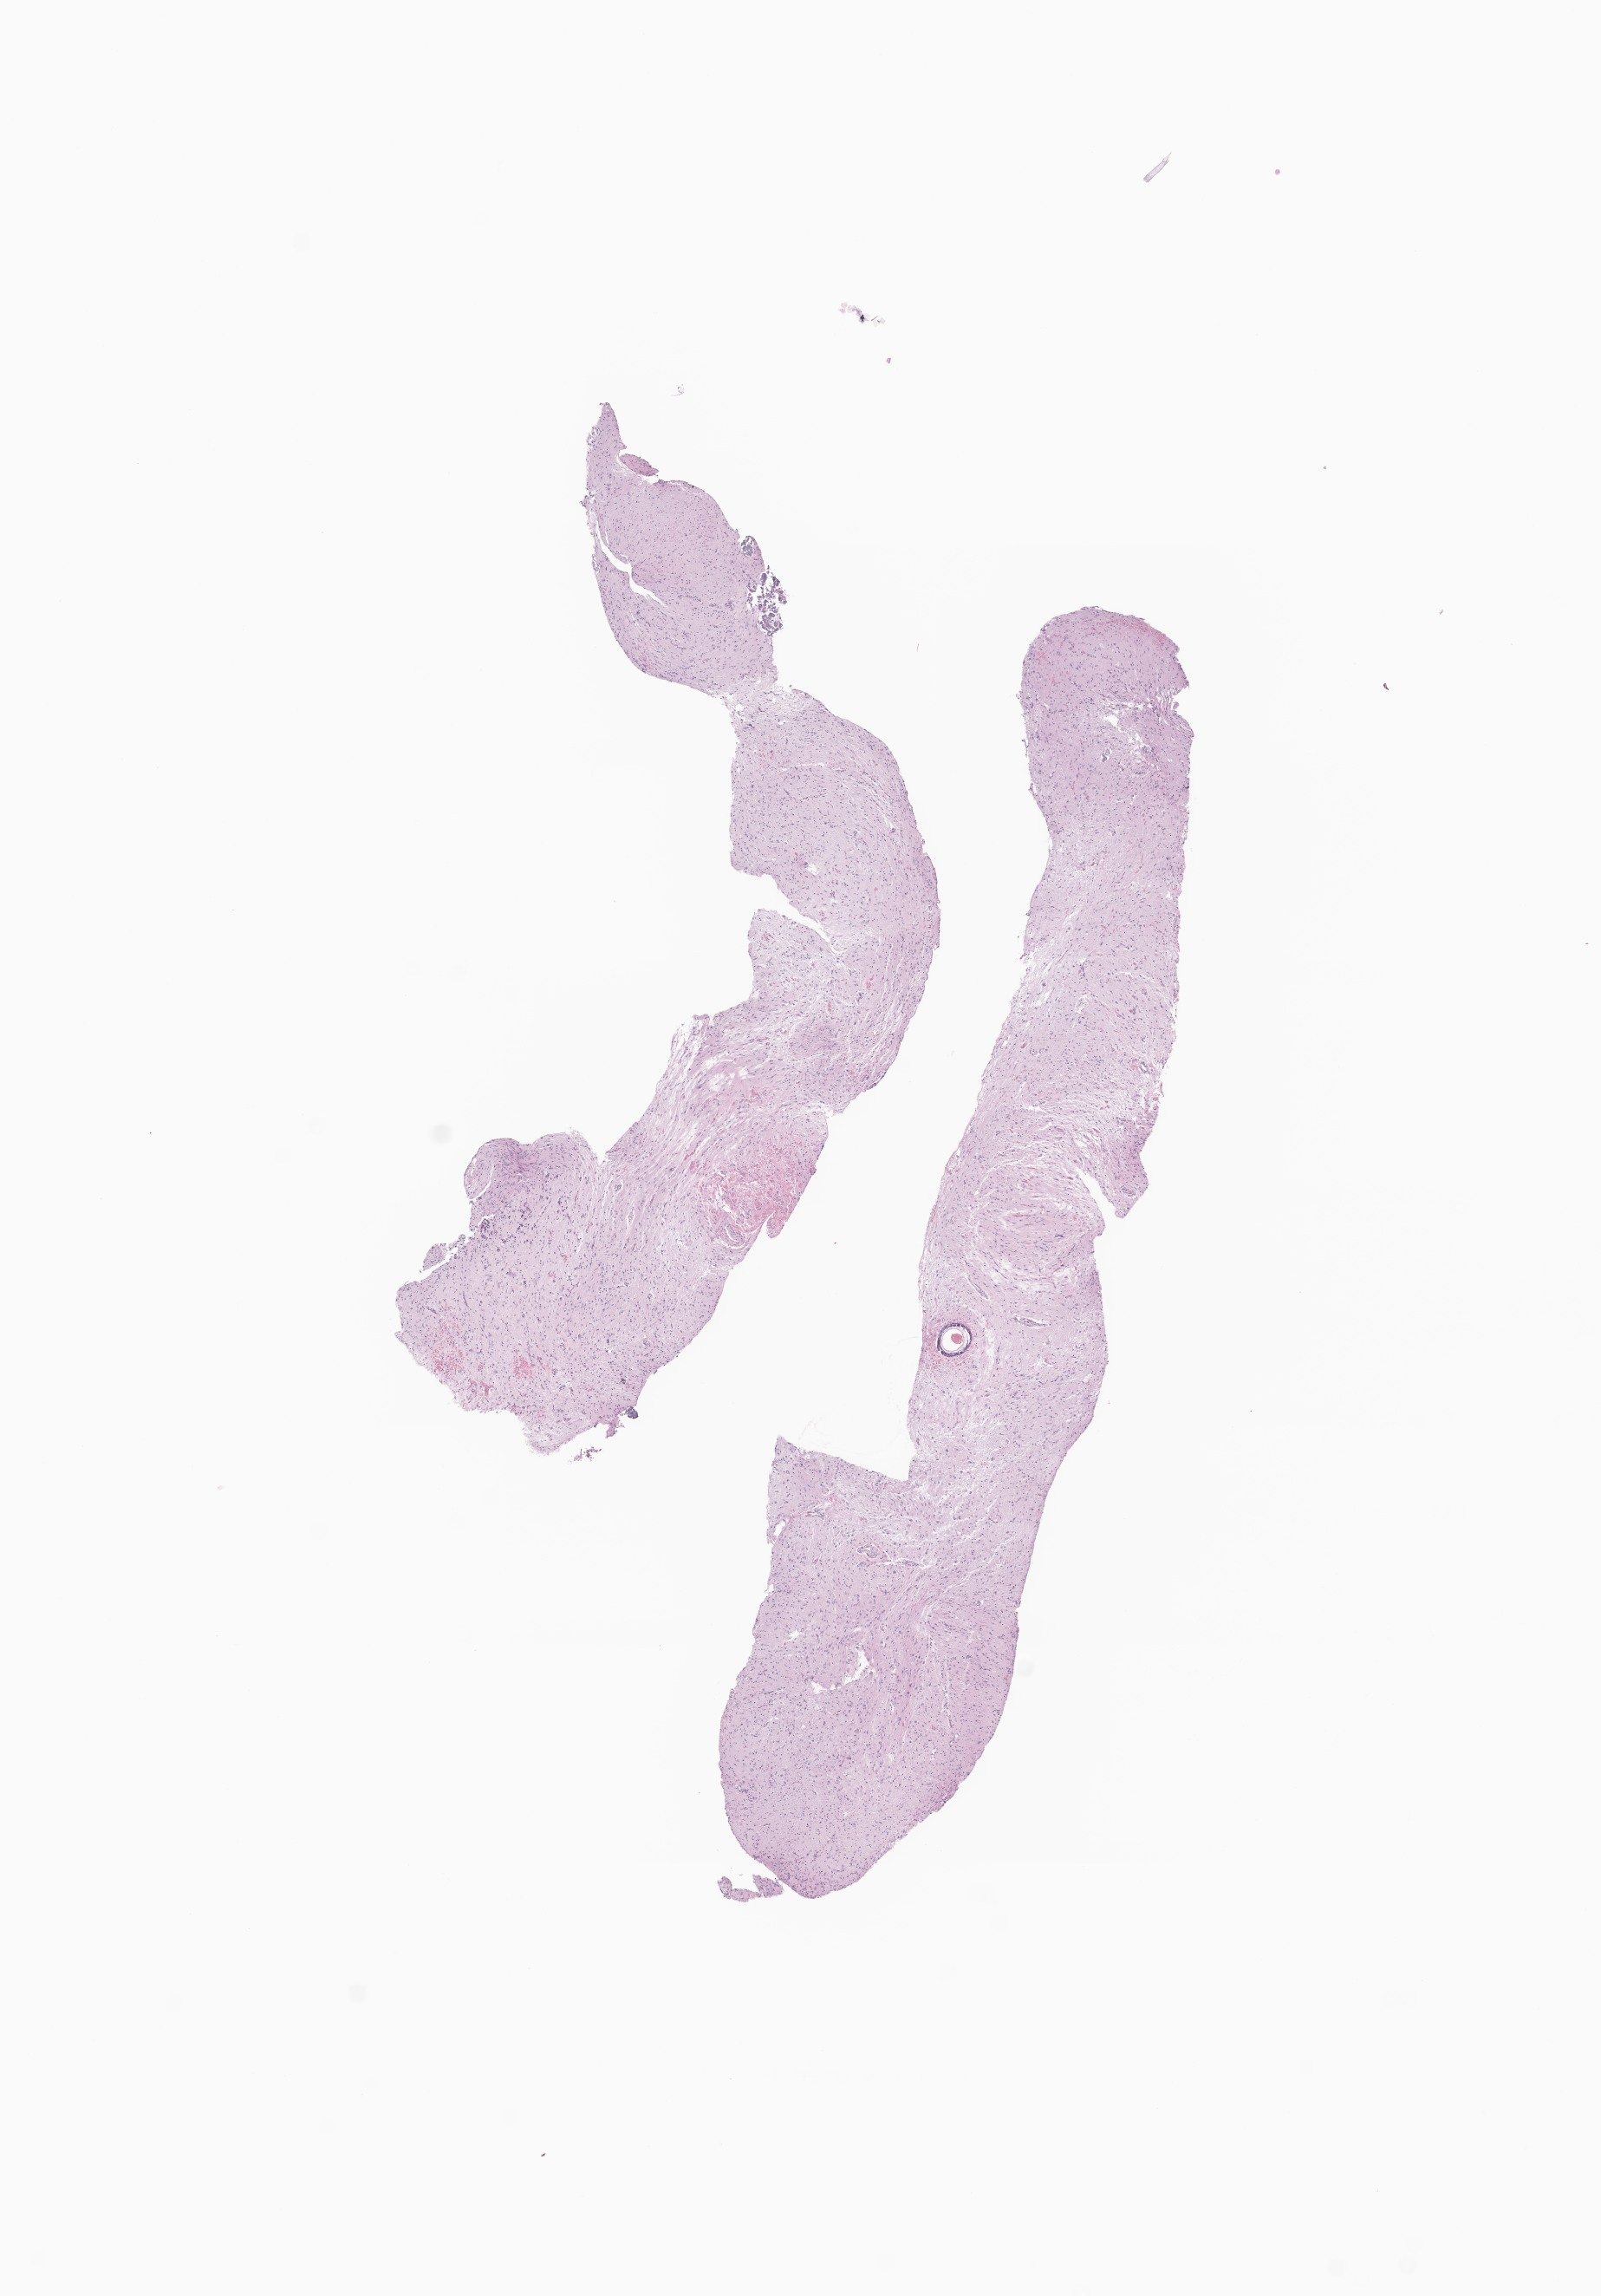
Digitized haematoxylin and eosin-stained section of tumor tissue from the brain, low-resolution overview of the scanned area, about 7.8 x 11.2 mm, formalin-fixed paraffin-embedded section. Patient: female, age 200 months (16 years 8 months).
Diagnosis (ICD-O-3 morphology term): Ganglioglioma, NOS.